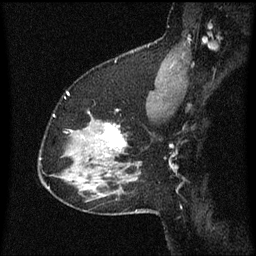
Breast MRI (dynamic contrast-enhanced), one sagittal slice. Slice 46 of 60 in the series (ordered by position). Dynamic contrast-enhanced series, image 2 of 3 at this slice position (ordered by acquisition). 1.5 T. TE 4.2 ms, TR 8.4 ms. 256 × 256 image matrix. Patient: female, 37 years. From the clinical record (not read from this slice): setting: breast cancer imaged before/during neoadjuvant chemotherapy; receptor status: HR-positive, HER2-negative.
Annotated regions visible in this slice (semi-automatic segmentation, software-assisted and operator-edited):
- analysis volume of interest (the breast-tissue region the enhancement analysis was run in; not a lesion): bounding box <94,120,129,157> (left, top, right, bottom; pixels)
- tumour enhancement mask (voxels above the 70 % enhancement threshold inside the analysis volume of interest): <102,124,127,157>